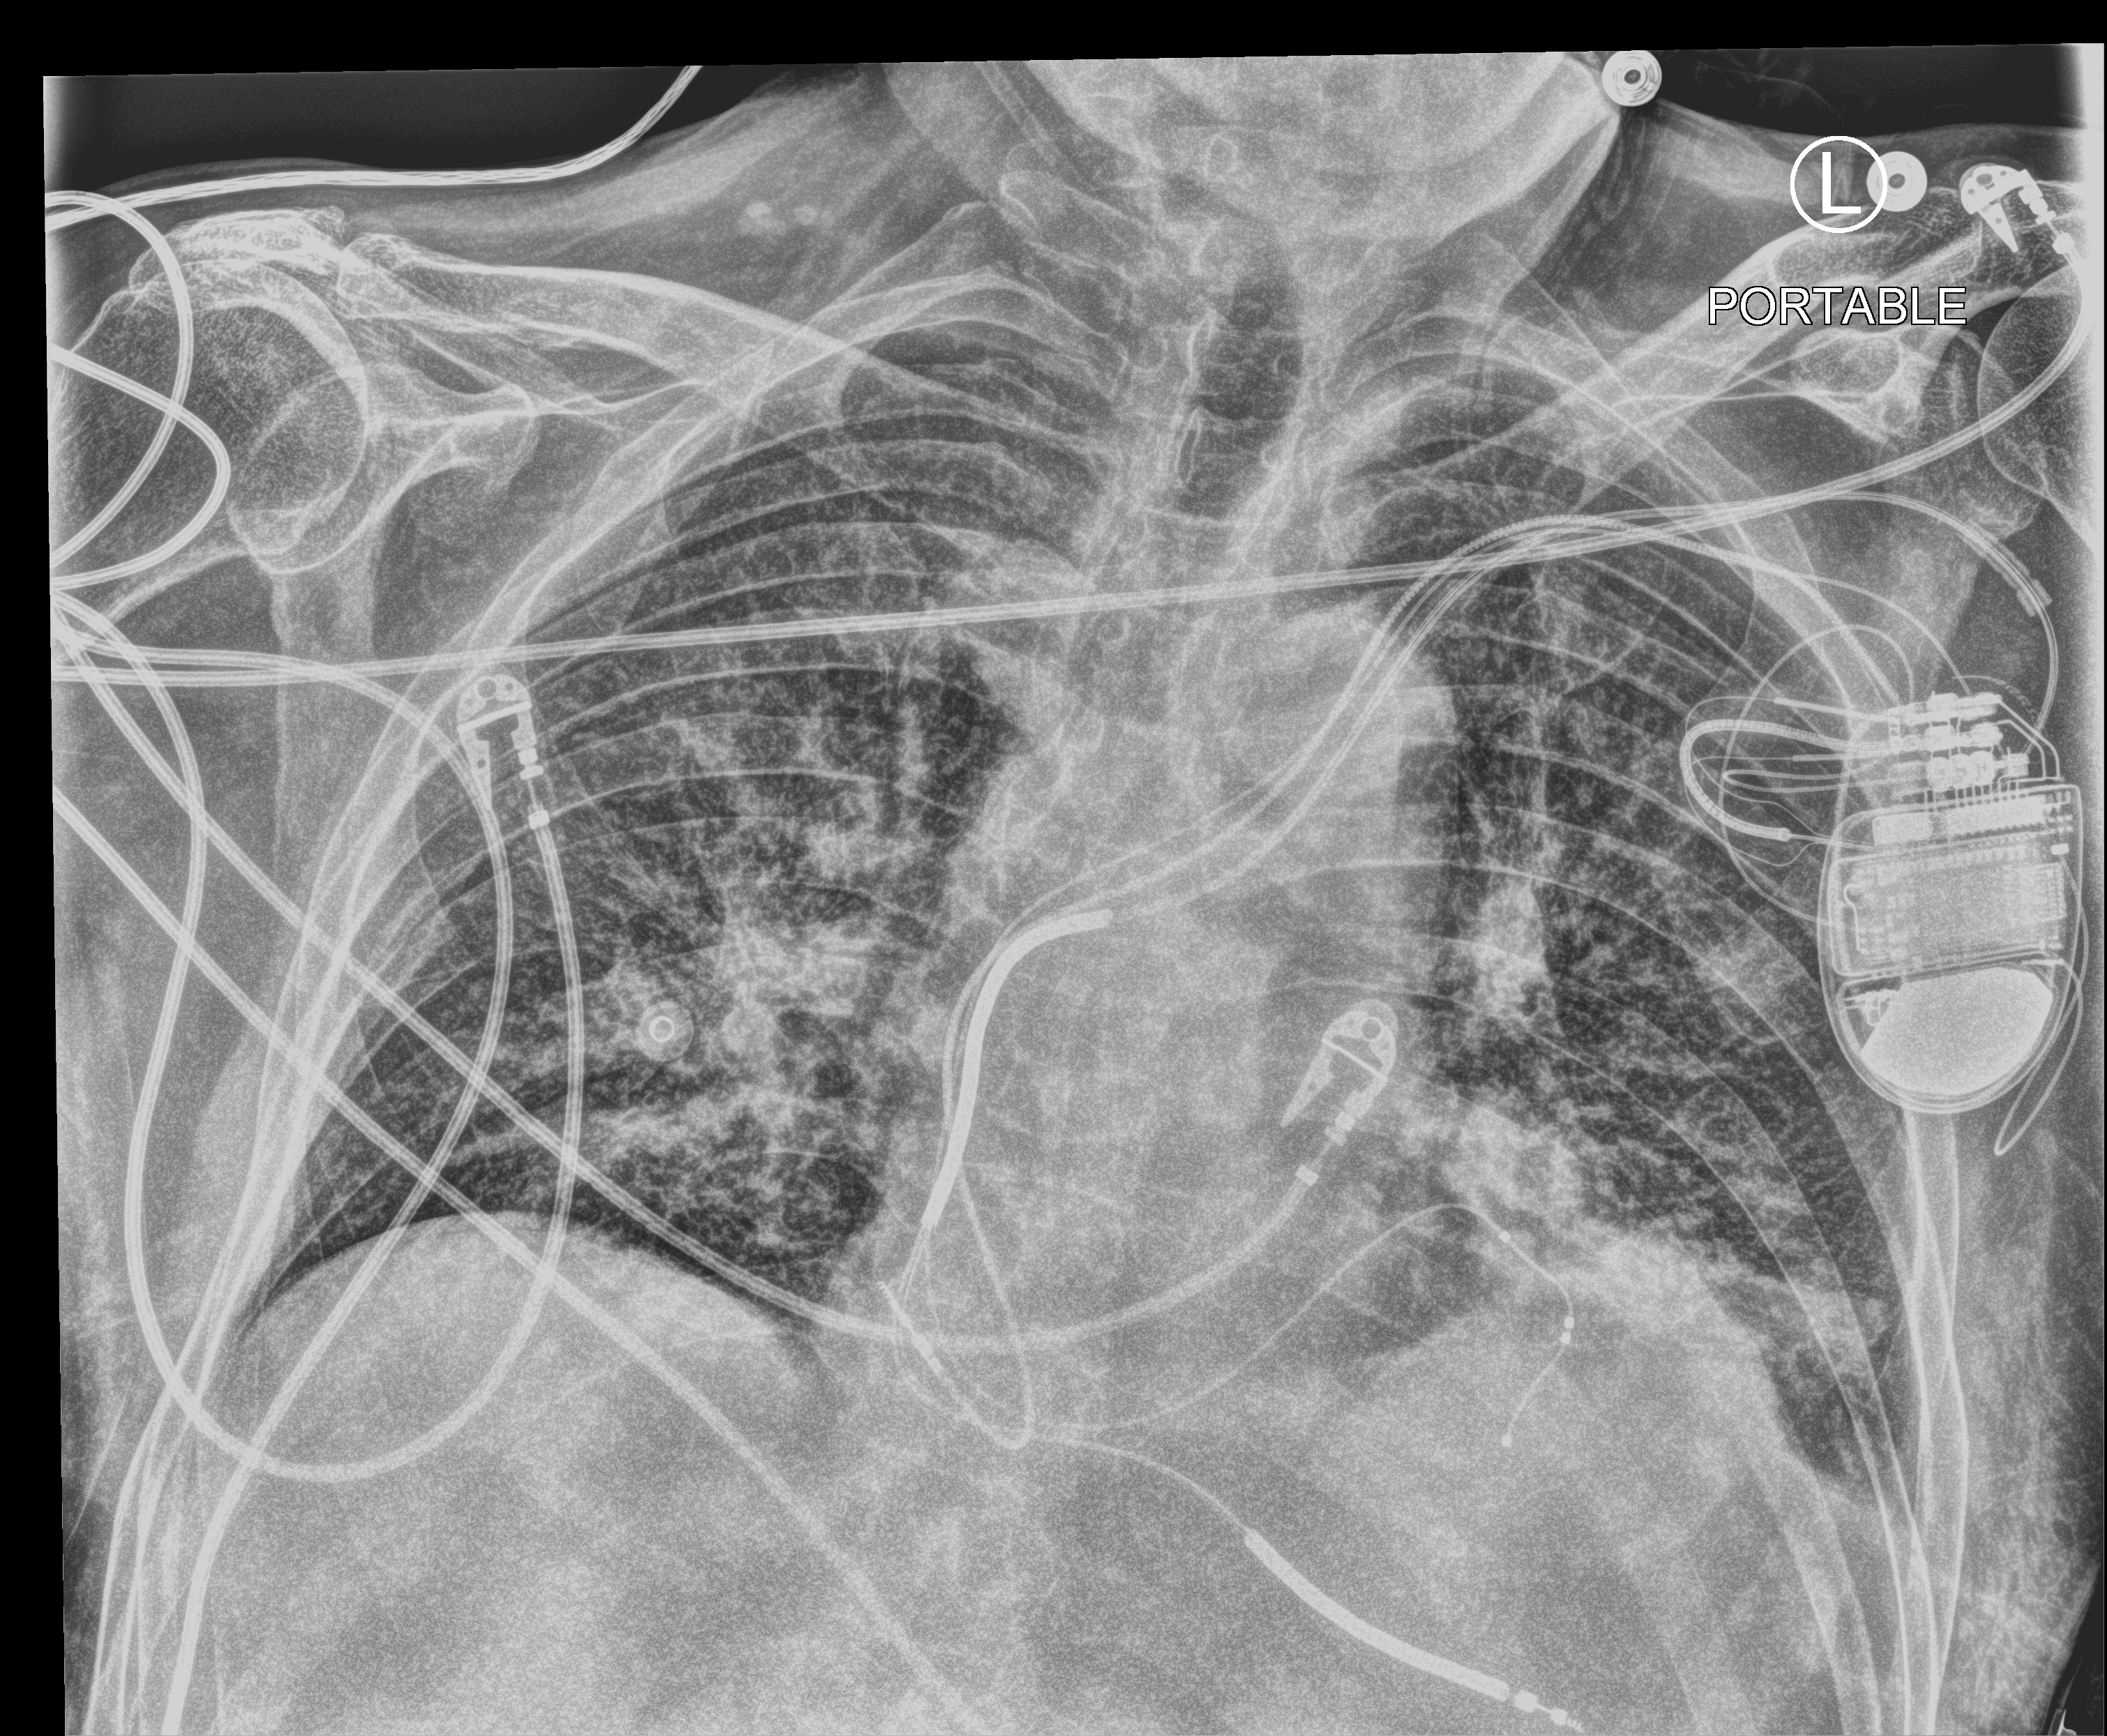
Portable chest radiograph. Male patient hospitalised with COVID-19, age 75–90 years.
From the hospital-stay record, not from the radiograph (when in the stay this image was taken is not recorded):
- mechanically ventilated during this hospital stay: no
- admitted to intensive care during this hospital stay: no